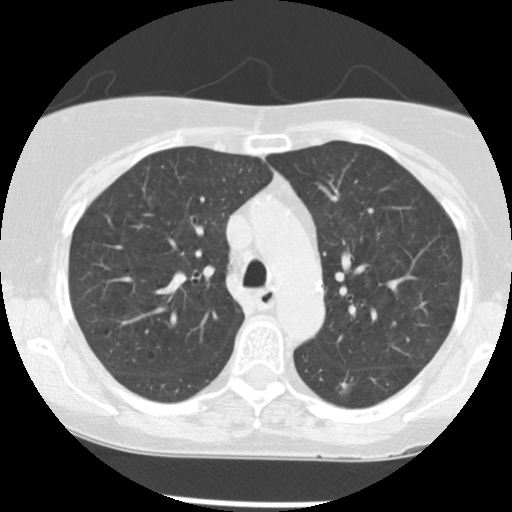
Axial slice from a low-dose chest CT screening exam. Second annual screen. Lung window (W 1500 / L -600 HU). 2.5 mm slice thickness. Standard (soft-tissue) reconstruction kernel (STANDARD). 512 × 512 image matrix, field of view 292 × 292 mm. Female participant, aged 63 years at enrolment. Current smoker at enrolment.
Expert-annotated lung lesion, bounding box [x1, y1, x2, y2] px = [326, 368, 366, 403]. Screening reader's record for this exam (one nodule recorded; not confirmed to be the boxed lesion): non-calcified nodule or mass ≥4 mm, left lower lobe, 7 × 6 mm, poorly defined margins, soft tissue attenuation, pre-existing on the prior screen: yes; interval growth: yes. Official screen result: positive, other. Later outcome: lung cancer diagnosed 460 days after this screen (after the third annual screen) — squamous cell carcinoma, NOS, left lower lobe, moderately differentiated (G2), stage IB (AJCC 6th edition), 15 mm at pathology.